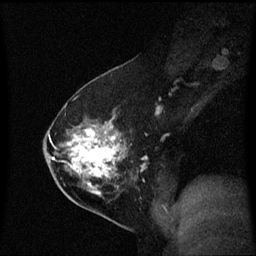
Breast MRI (dynamic contrast-enhanced), one sagittal slice; slice 35 of 60 in the series (ordered by position); dynamic contrast-enhanced series, image 2 of 3 at this slice position (ordered by acquisition); 1.5 T; TE 4.2 ms, TR 8.4 ms; 2 mm slice thickness; 256 × 256 image matrix, field of view 210 × 210 mm. Patient: female, 54 years. Case-level facts recorded for this patient, not image findings: setting: breast cancer imaged before/during neoadjuvant chemotherapy; receptor status: HER2-positive.
Annotated regions visible in this slice (semi-automatically segmented with operator editing):
- analysis volume of interest (the breast-tissue region the enhancement analysis was run in; not a lesion): bounding box (x1, y1, x2, y2) in pixels: (59, 117, 139, 199)
- tumour enhancement mask (voxels above the 70 % enhancement threshold inside the analysis volume of interest): (69, 124, 123, 195)